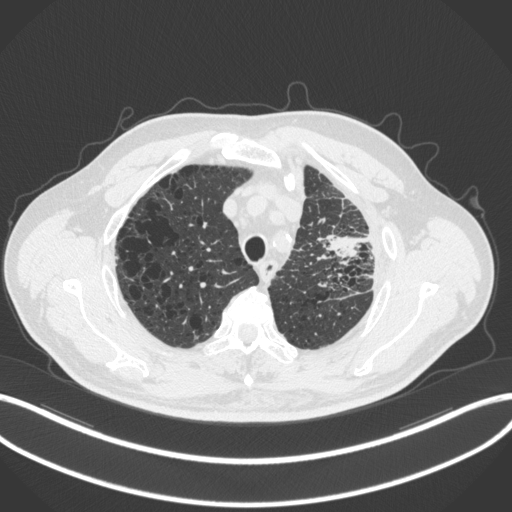
Chest CT, one axial slice; slice 248 of 286 in the series (ordered by position); reconstruction kernel B31f; 120 kVp; lung window (W 1500 / L -600 HU); 1 mm slice thickness; 512 × 512 image matrix. Male patient, age 68 years. From the clinical record (not read from this slice): clinical TNM (as recorded): T3 N3 M1.
Annotated regions visible in this slice (rectangle marked by the reading radiologist):
- lung tumour (recorded histology: adenocarcinoma): box from (x=317, y=226) to (x=360, y=265) px